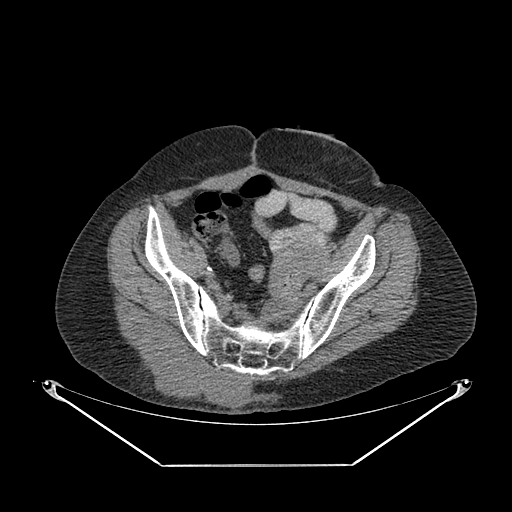
CT of an extremity soft-tissue mass (from a PET/CT study), one axial slice; position 70 of 267 along the scan axis; 140 kVp; soft-tissue window (W 400 / L 40 HU); 3.75 mm slice thickness; 512 × 512 image matrix, field of view 500 × 500 mm. Female patient. From the clinical record (not read from this slice): histological type: spindle cell suggestive of myxofibrosarcoma; grade: intermediate; site of the primary tumour: right buttock.
Structures marked on this image (expert contour drawn on MRI and transferred to this co-registered scan by the dataset authors):
- gross tumour volume (mass): bounding box (x1, y1, x2, y2) in pixels: (130, 338, 250, 407)